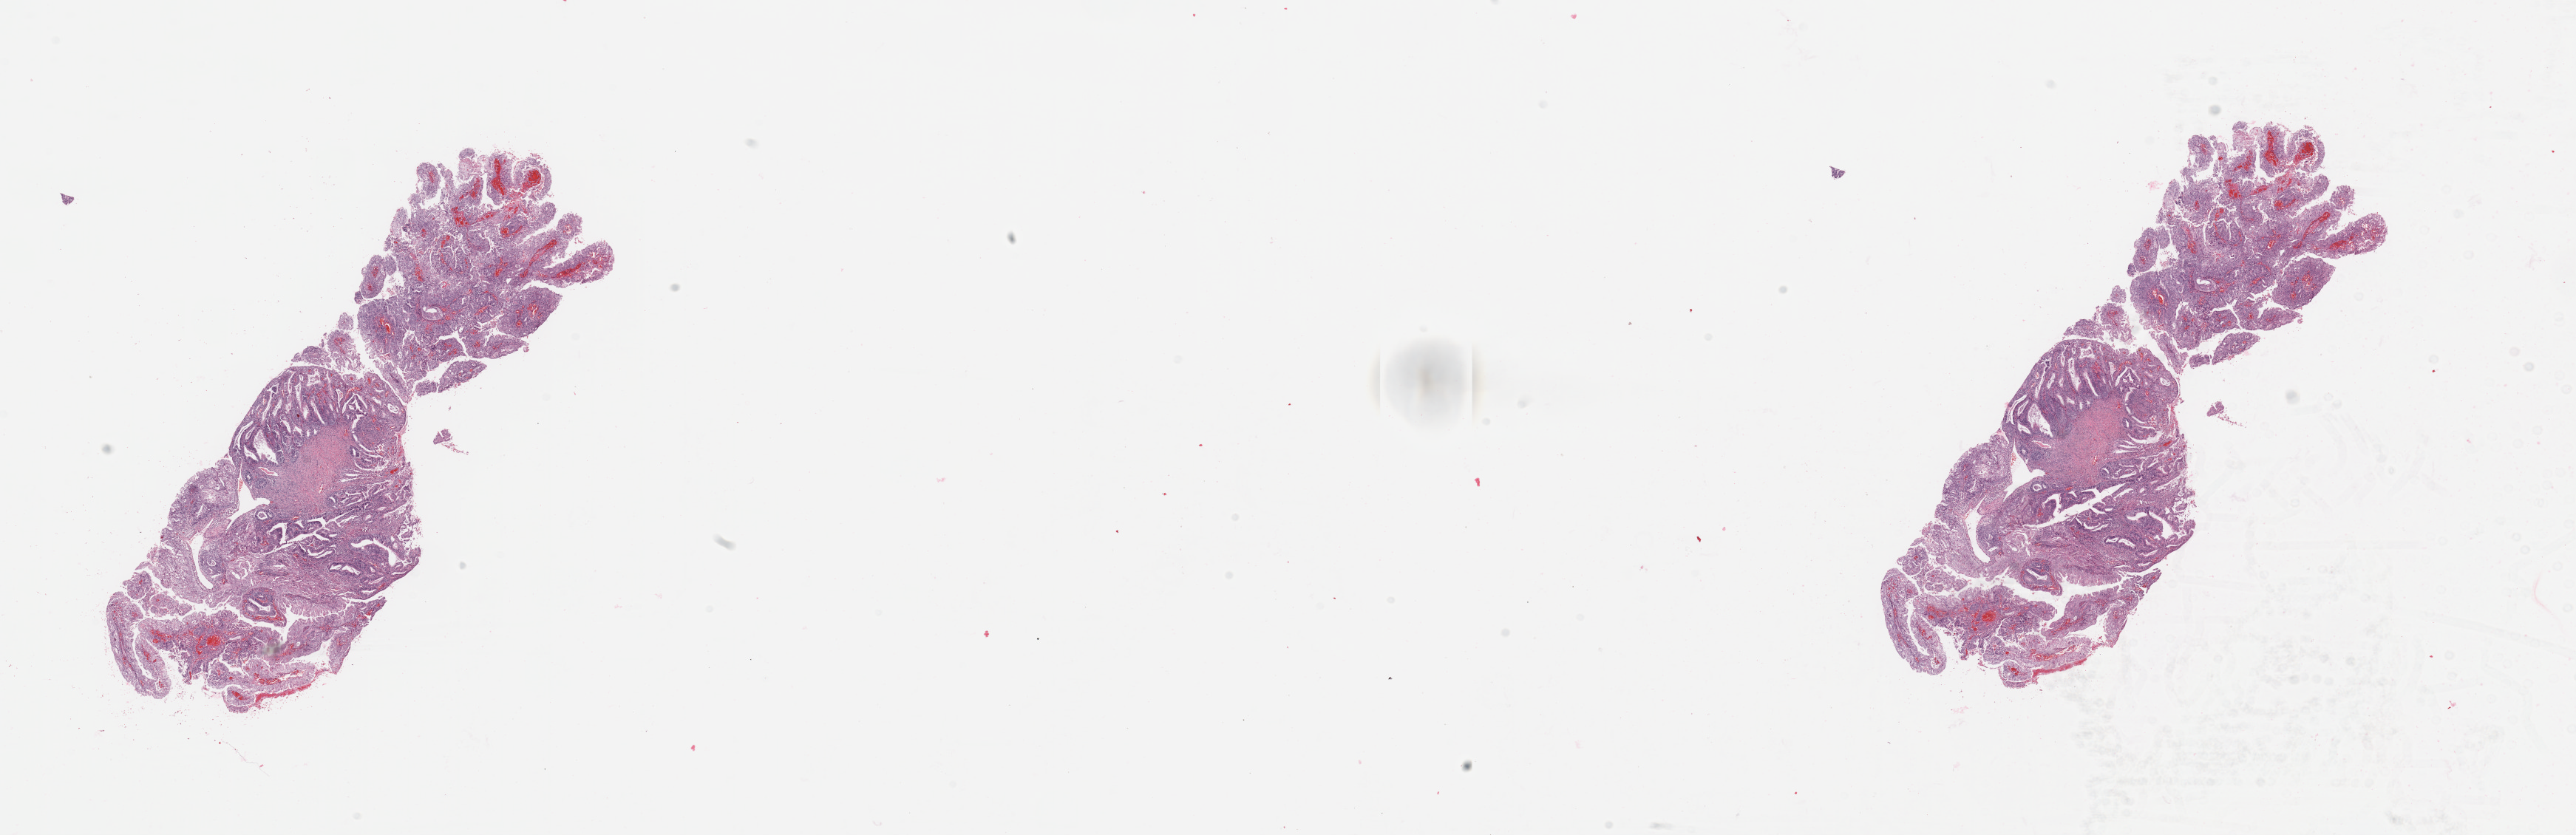
H&E whole-slide image, low-resolution overview of the scanned area, about 27.6 x 8.9 mm. Tumour tissue sample, sampled site: uterus. Patient: female, age 74 years.
Histologic diagnosis: Endometrioid adenocarcinoma, NOS.